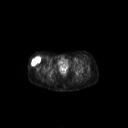
FDG PET of an extremity soft-tissue mass (from a PET/CT study), one axial slice; position 59 of 267 along the scan axis; 3.27 mm slice thickness; 128 × 128 image matrix. Female patient, age 34 years. Case-level facts recorded for this patient, not image findings: histological type: synovial sarcoma; grade: intermediate; site of the primary tumour: right thigh.
Structures marked on this image (expert contour drawn on MRI and transferred to this co-registered scan by the dataset authors):
- gross tumour volume including surrounding oedema: bounding box [x1, y1, x2, y2] px = [30, 56, 40, 66]
- gross tumour volume (mass): [30, 56, 40, 66]